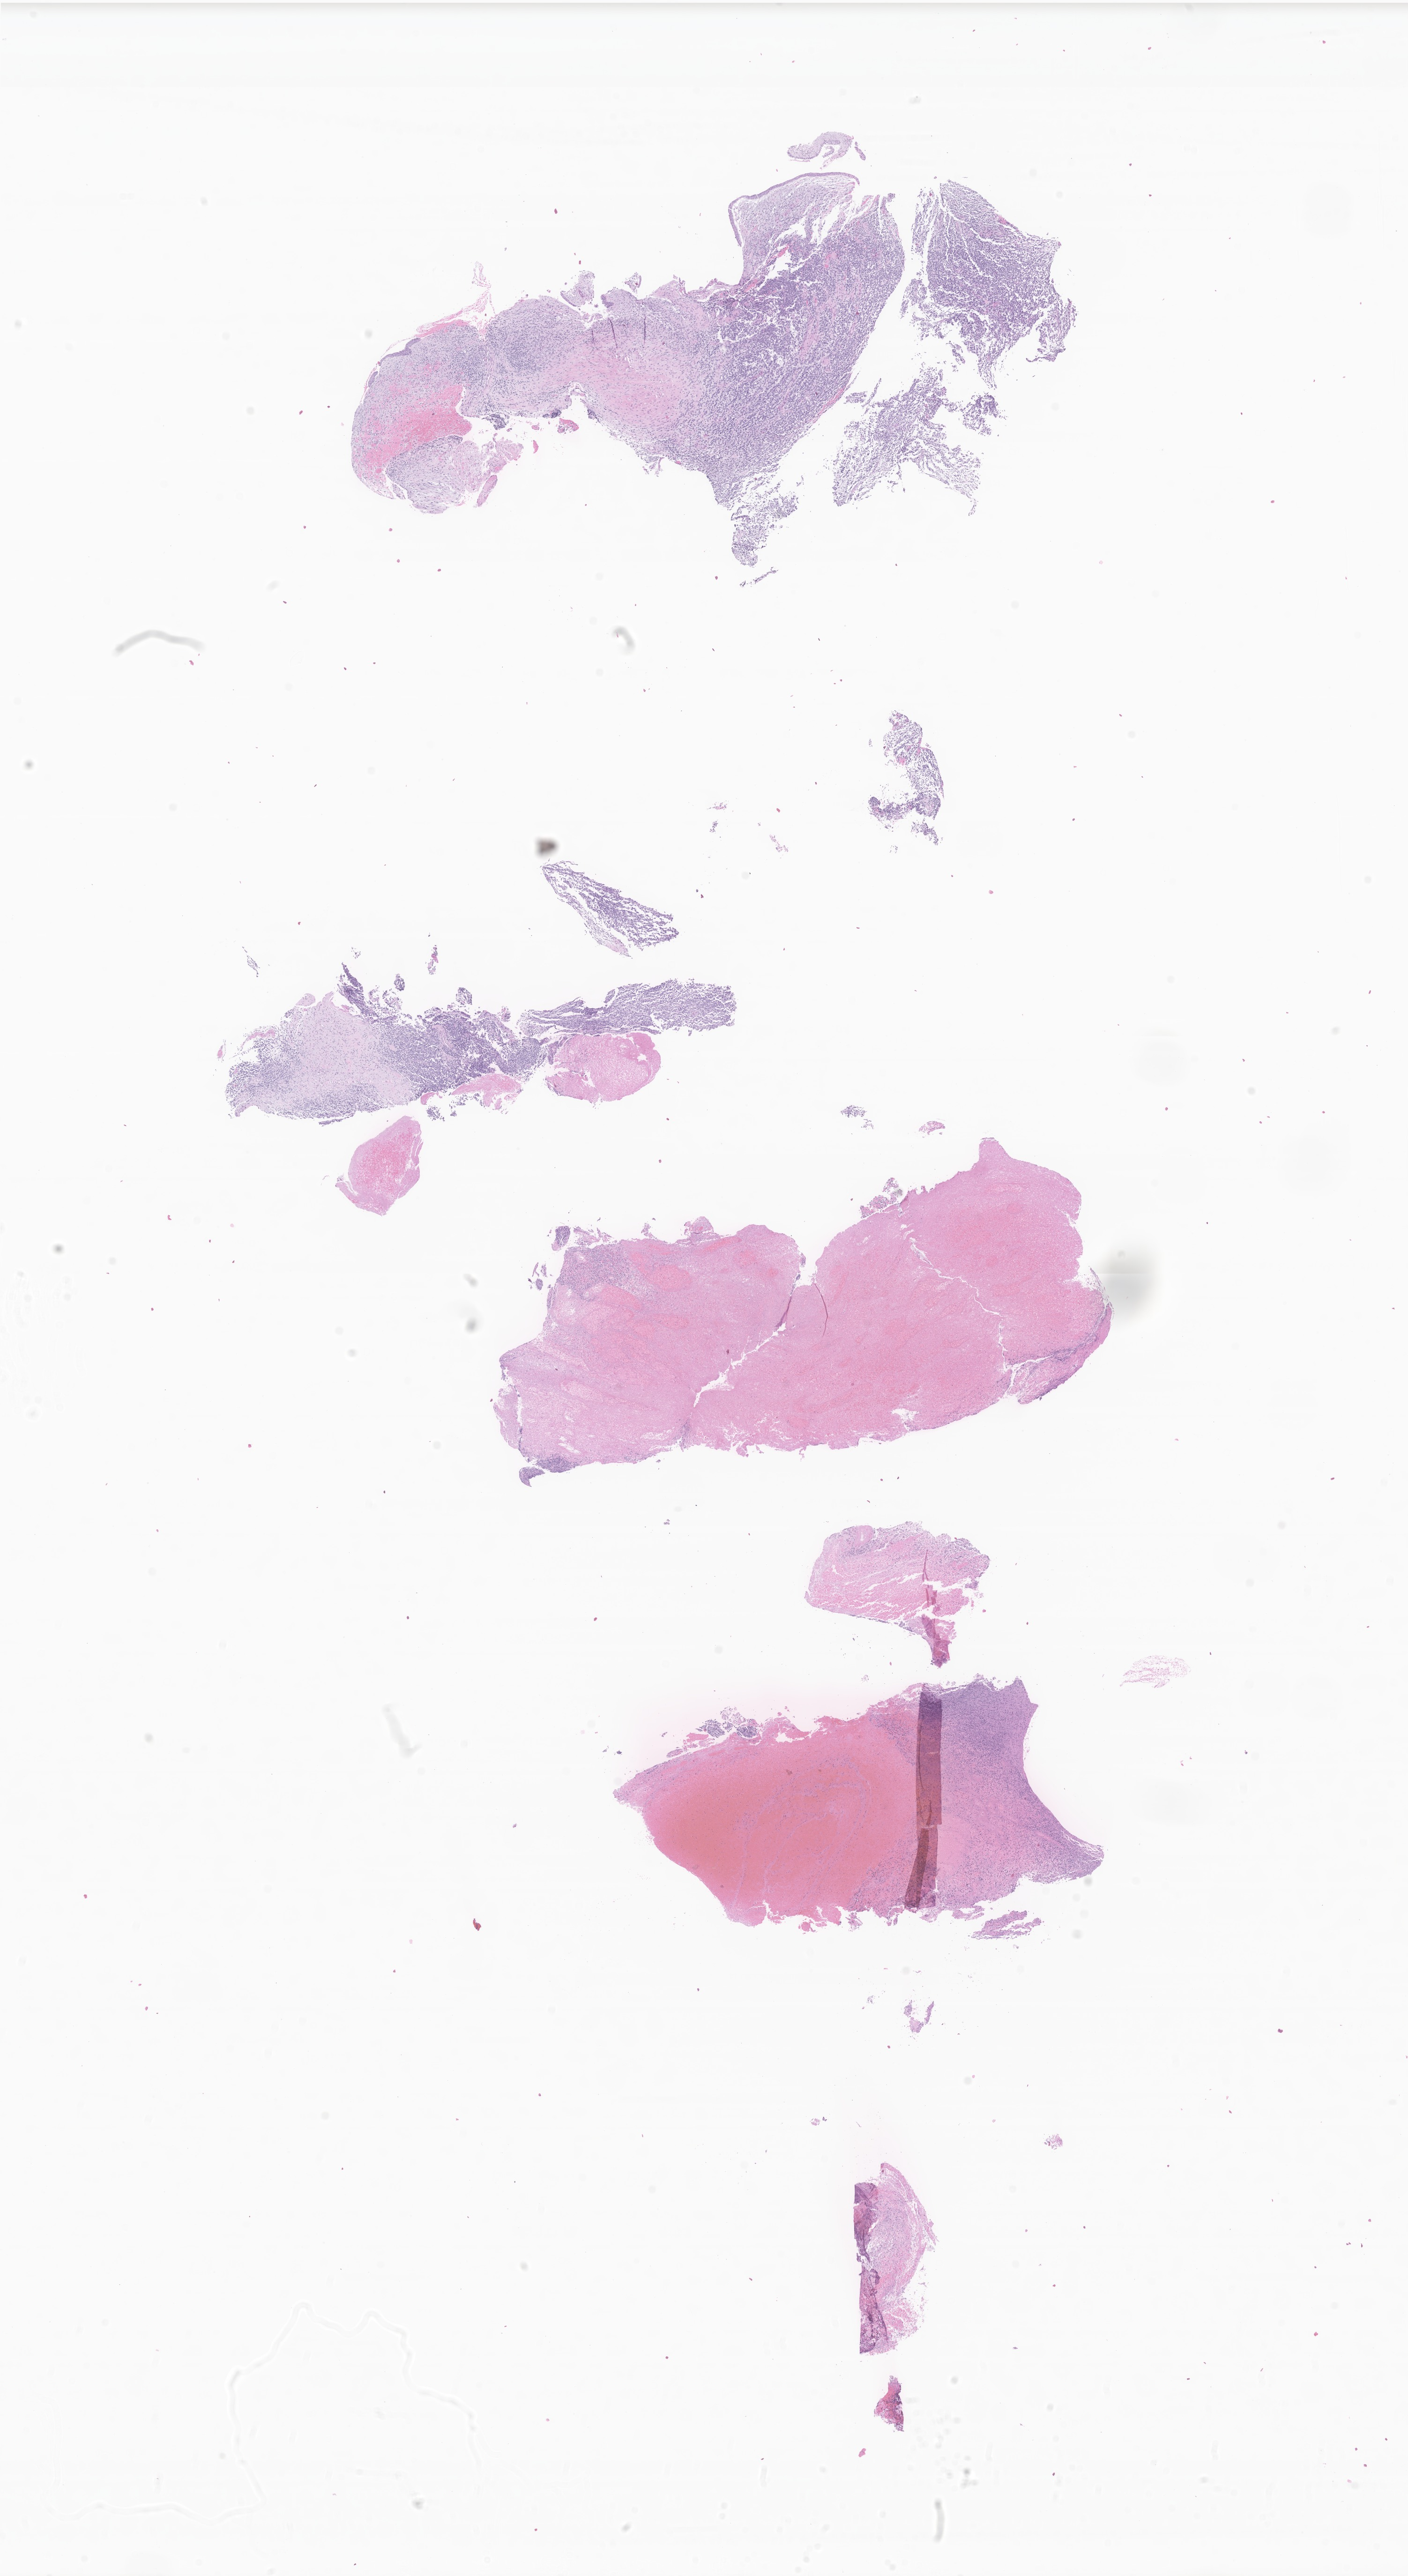
Digitized hematoxylin and eosin (H&E)-stained section of tumor tissue from the nasal cavity, whole scanned area (about 12.7 x 23.2 mm) shown as a low-resolution overview. Formalin-fixed, paraffin-embedded (FFPE) tissue. Male patient, age 730 days (about 2.0 years).
Diagnosis (ICD-O-3 morphology term): Rhabdomyosarcoma, NOS.